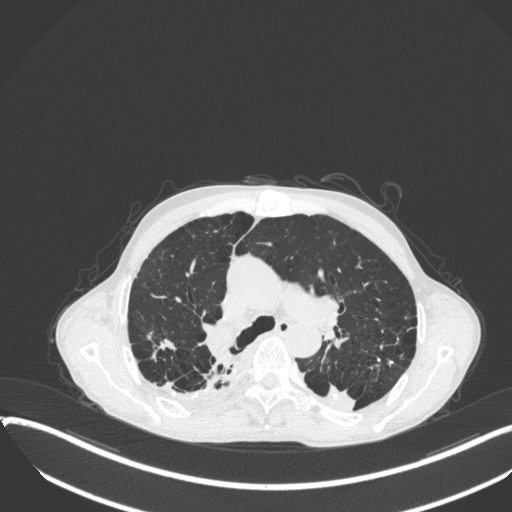
Chest CT, one axial slice; position 259 of 400 along the scan axis; reconstruction kernel B31f; lung window (W 1500 / L -600 HU); 512 × 512 image matrix, field of view 400 × 400 mm. Male patient, age 57 years. Case-level facts recorded for this patient, not image findings: clinical TNM (as recorded): T4 N0 M0.
Structures marked on this image (rectangle marked by the reading radiologist):
- lung tumour (recorded histology: squamous cell carcinoma): bounding box (x1, y1, x2, y2) in pixels: (307, 381, 358, 418)